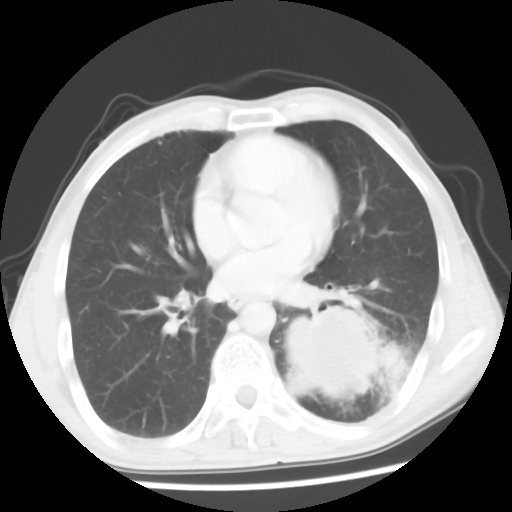
Chest CT, one axial slice. Position 26 of 56 along the scan axis. Reconstruction kernel STANDARD. Lung window (W 1500 / L -600 HU). 5 mm slice thickness. 512 × 512 image matrix, field of view 318 × 318 mm. Male patient, age 60 years. Case-level facts recorded for this patient, not image findings: clinical TNM (as recorded): T4 N0 M0.
Structures marked on this image (bounding box drawn by a radiologist):
- lung tumour (recorded histology: squamous cell carcinoma): box from (x=267, y=290) to (x=413, y=419) px